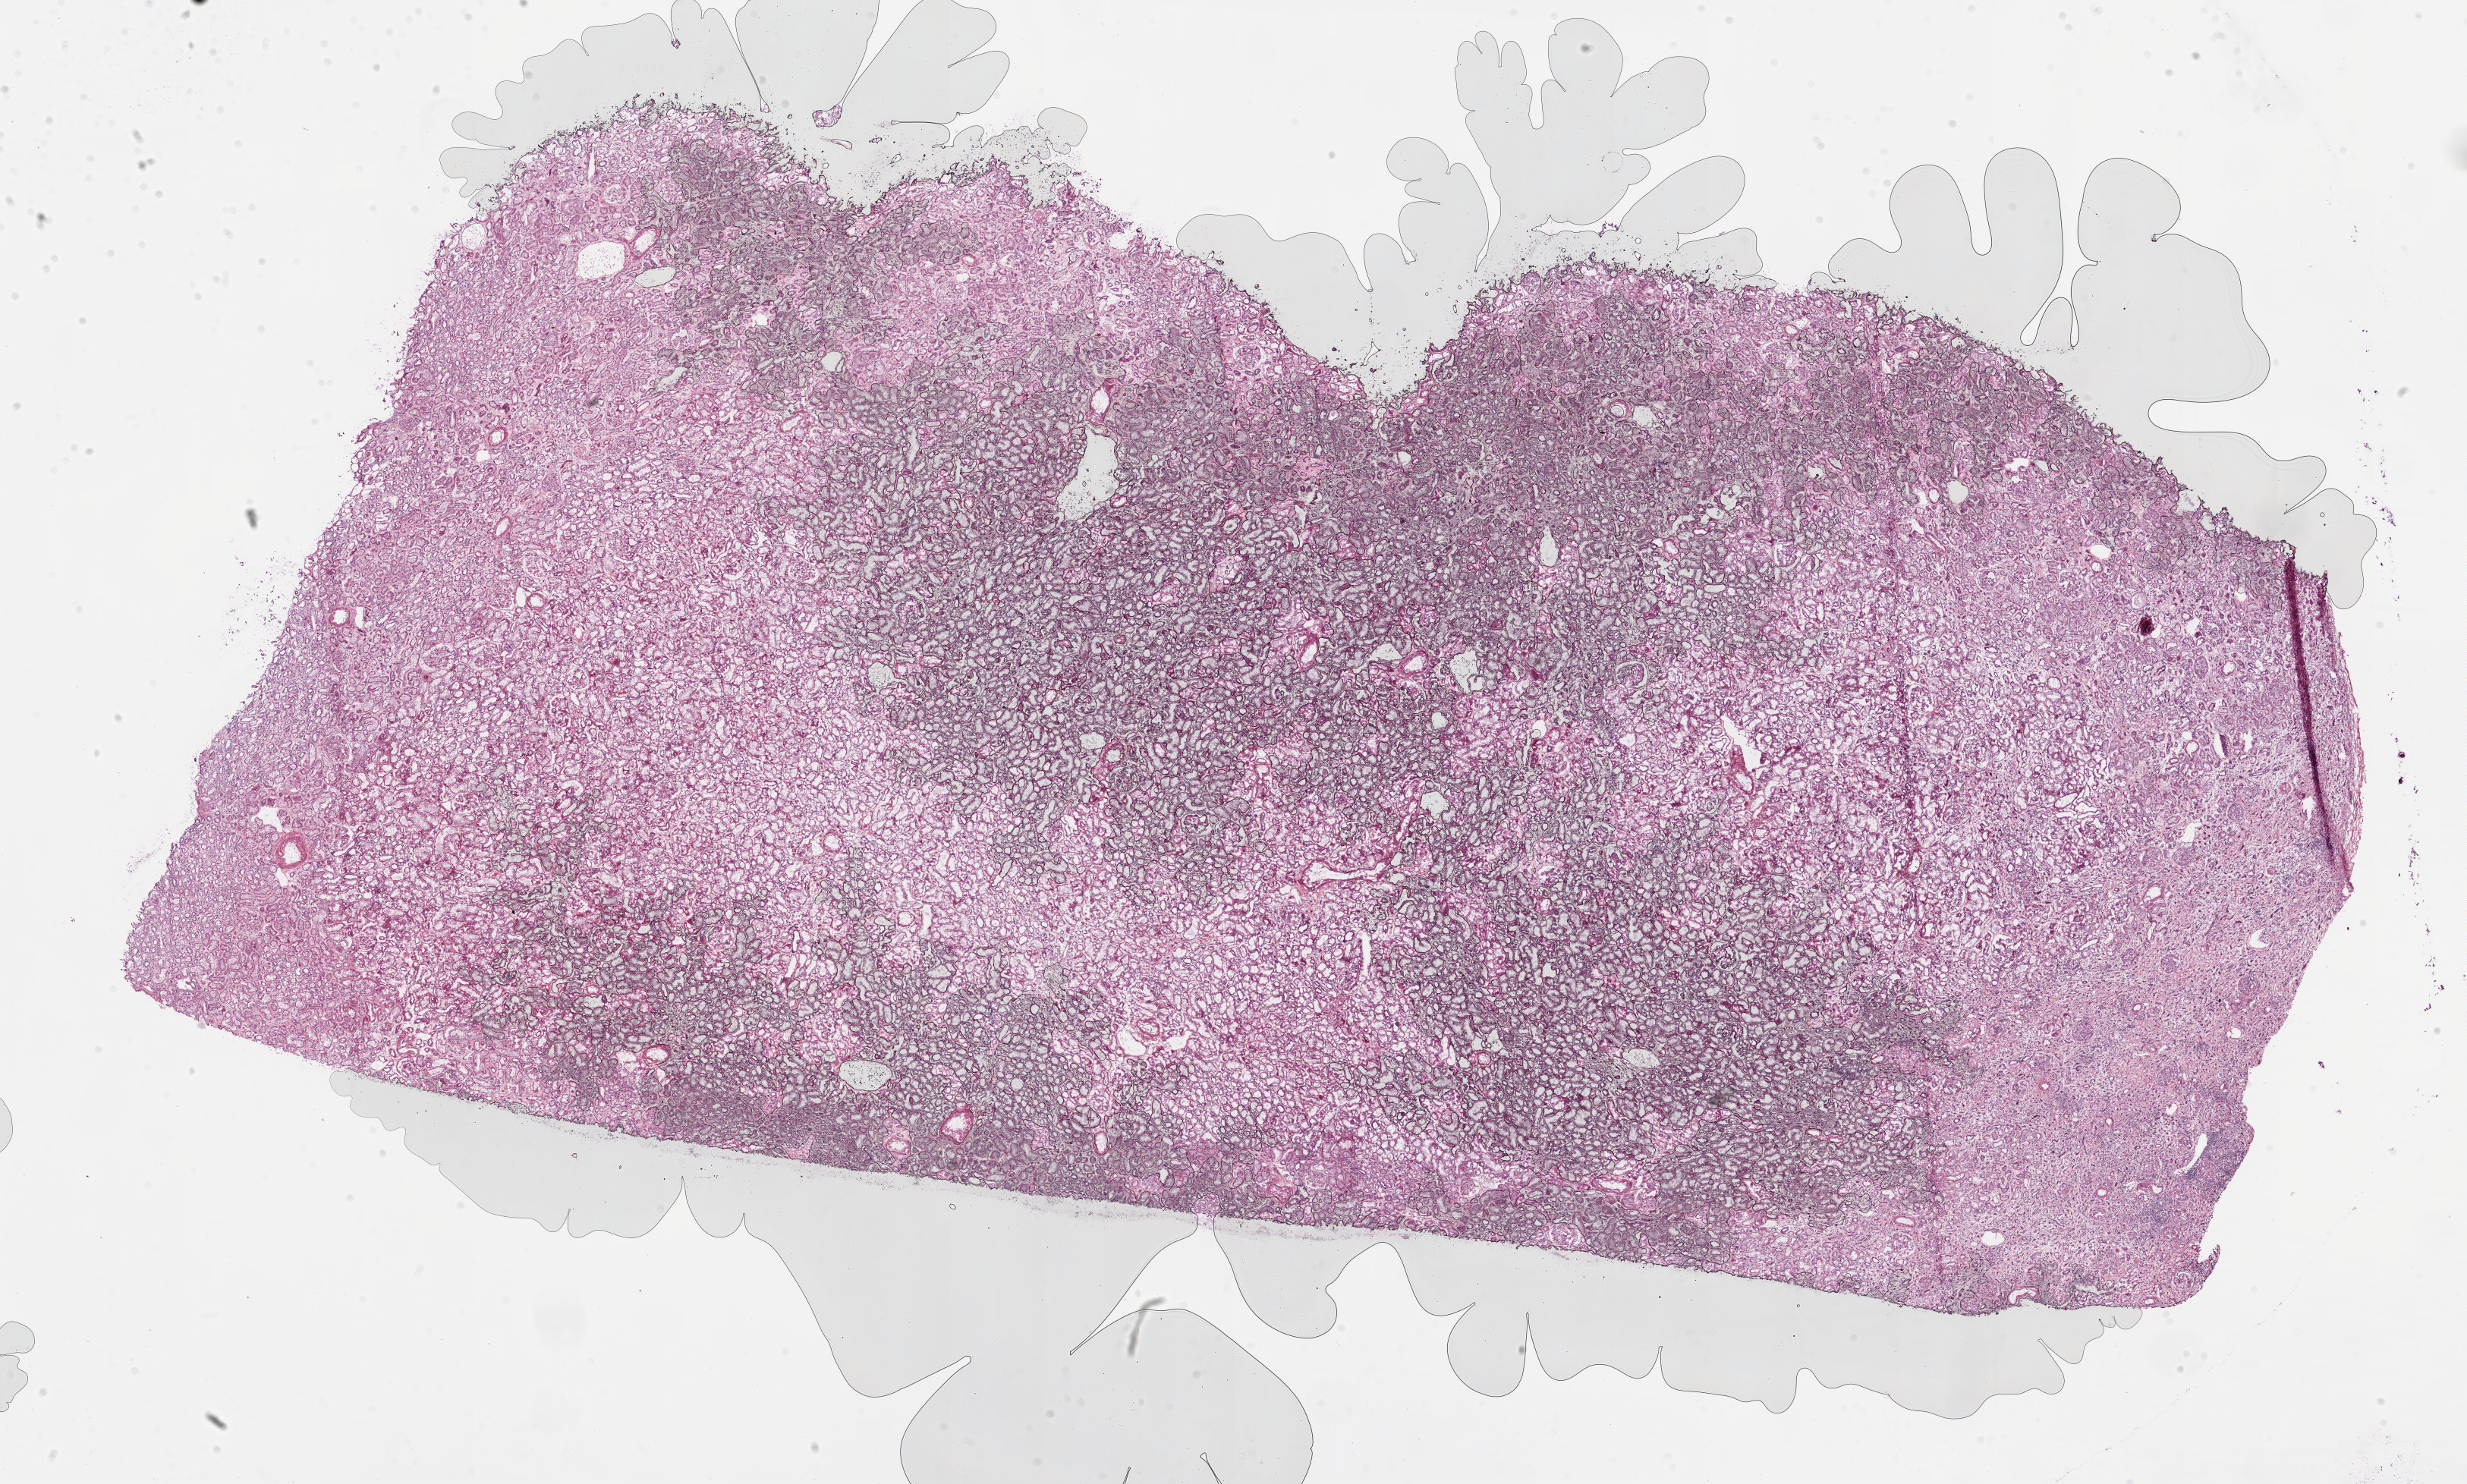
Digitized H&E-stained tissue section (whole slide), shown as a low-resolution overview of the whole scanned area (about 25.8 x 15.5 mm, slide scanned at 20x), frozen section, solid tissue normal (non-tumour tissue) sample from the kidney. Patient: male, age at initial diagnosis 61 years.
This section: solid tissue normal sample (biorepository sample class). Patient diagnosis: Clear cell adenocarcinoma, NOS.